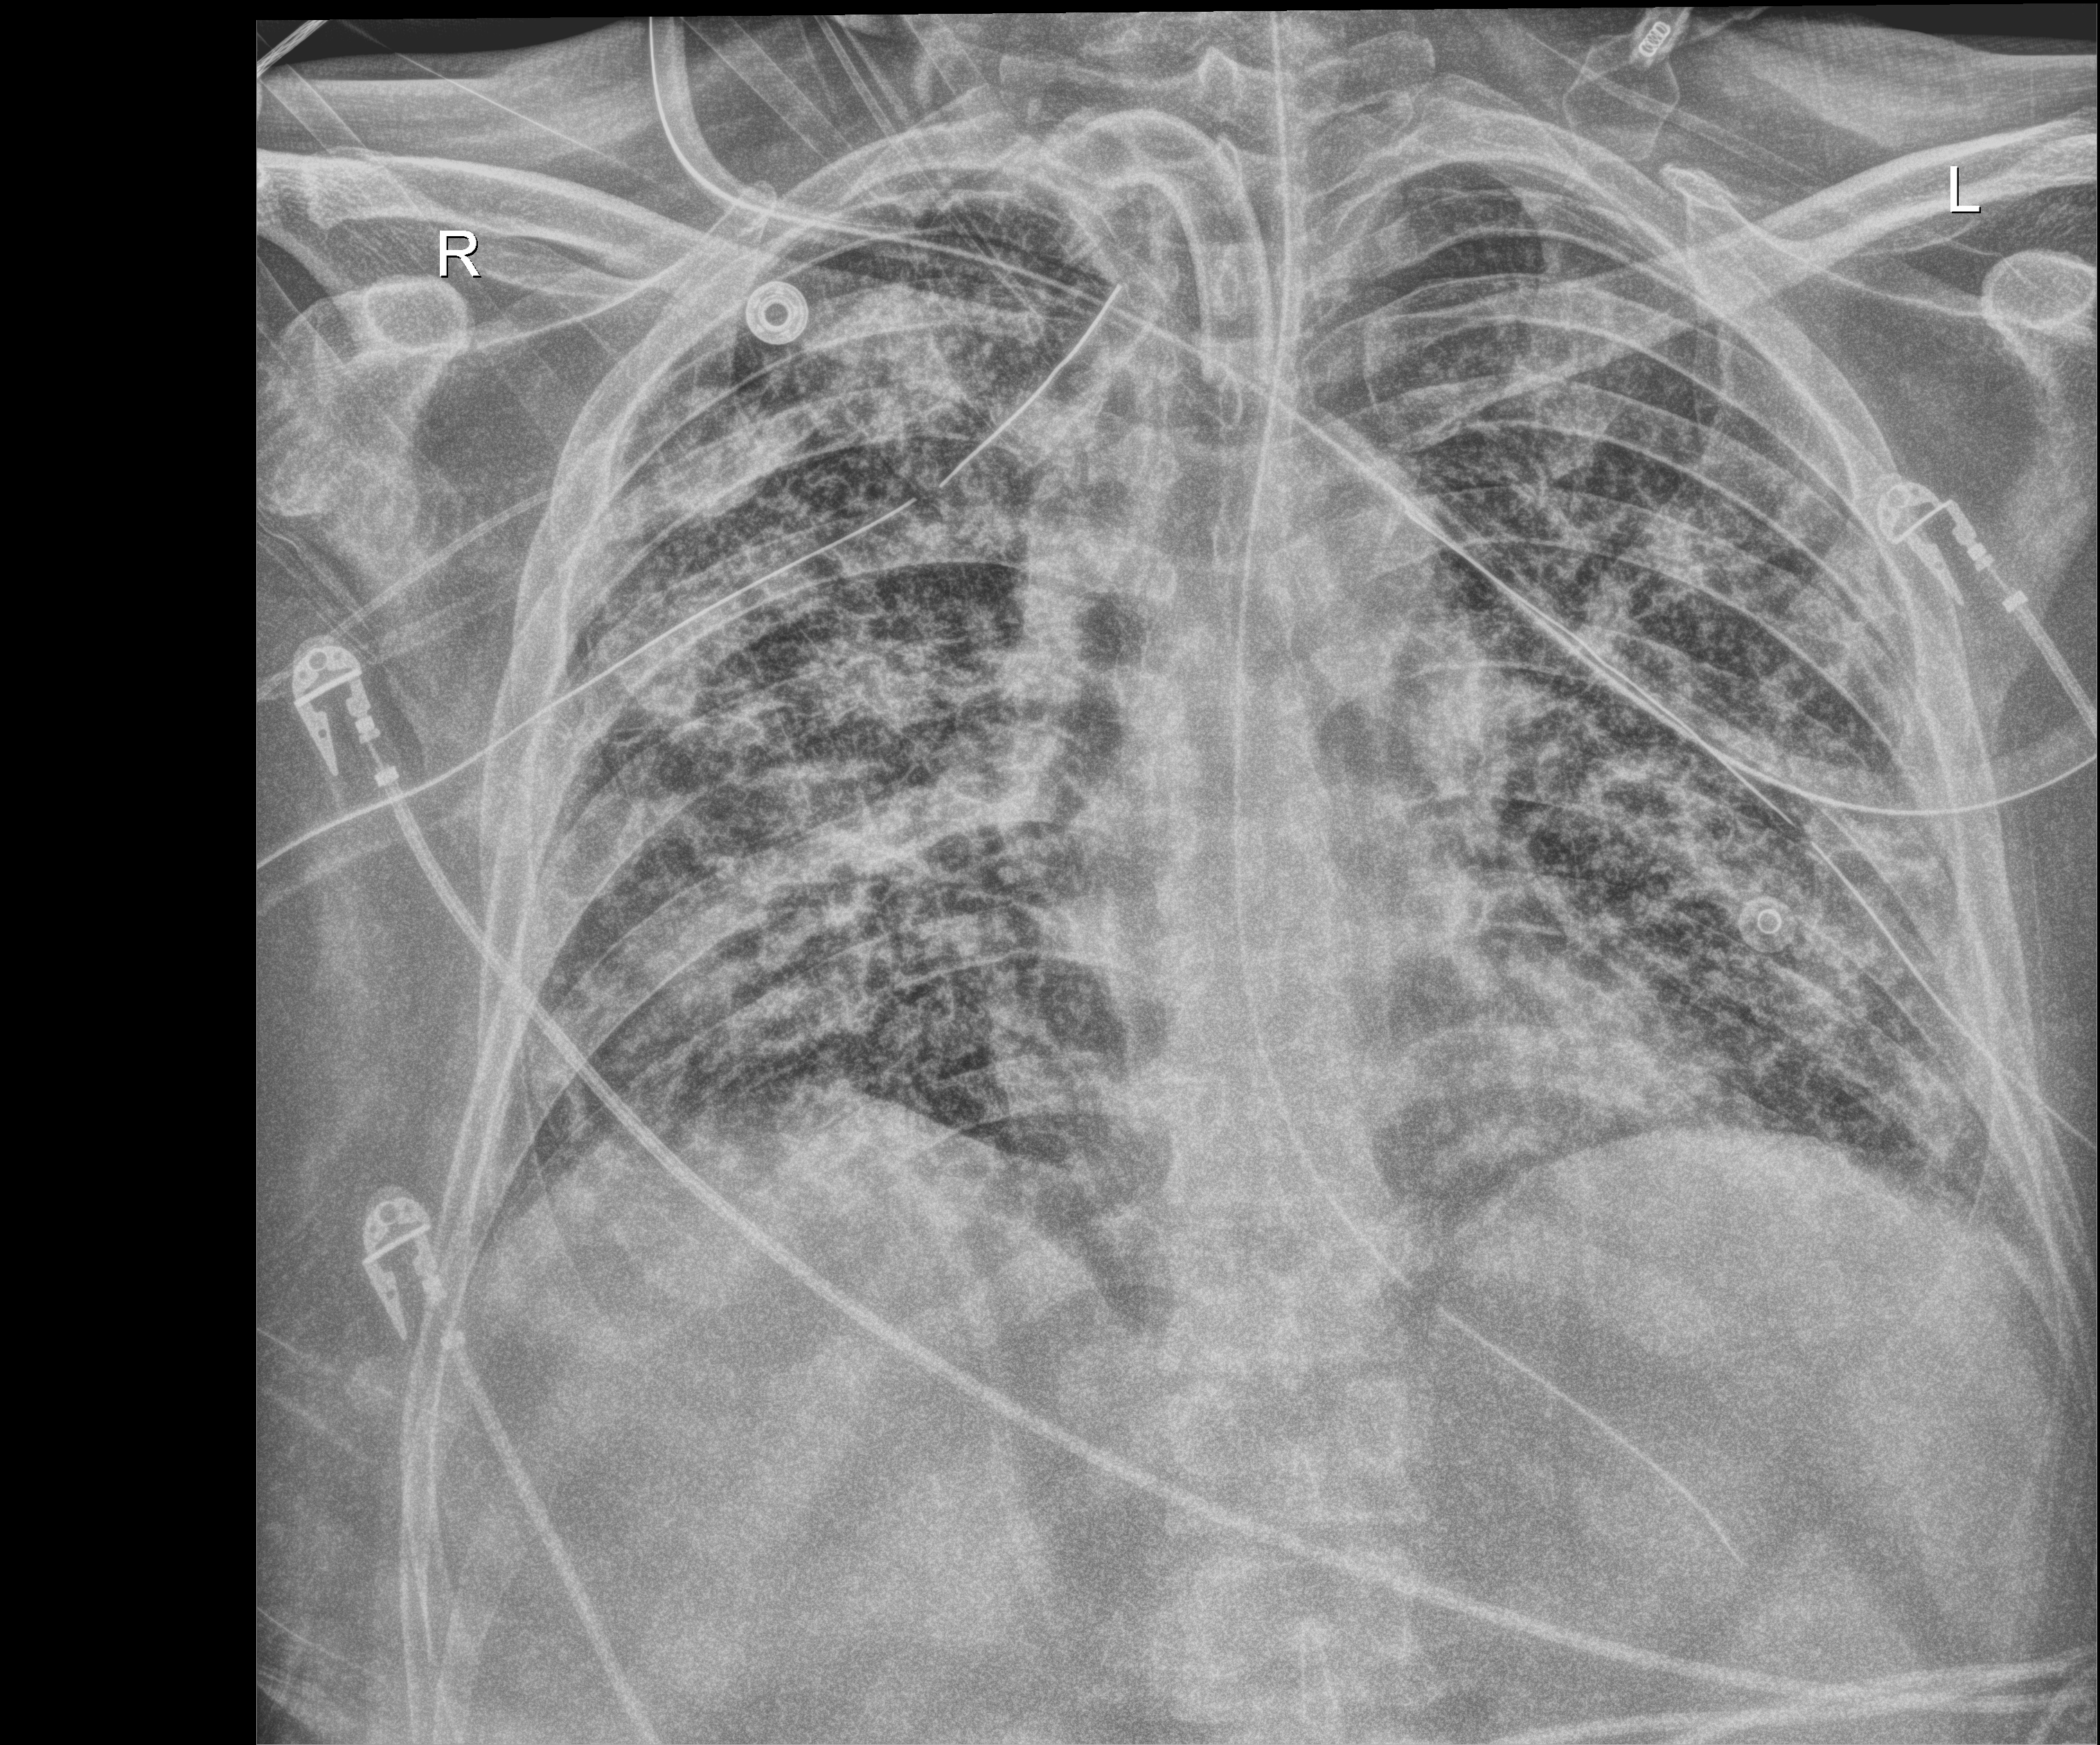
Chest X-ray (portable); anteroposterior (AP) projection. Patient hospitalised with COVID-19; male, aged 18–59 years.
From the hospital-stay record, not from the radiograph (when in the stay this image was taken is not recorded):
- mechanically ventilated during this hospital stay: yes
- admitted to intensive care during this hospital stay: yes
- diabetes (admission record): yes